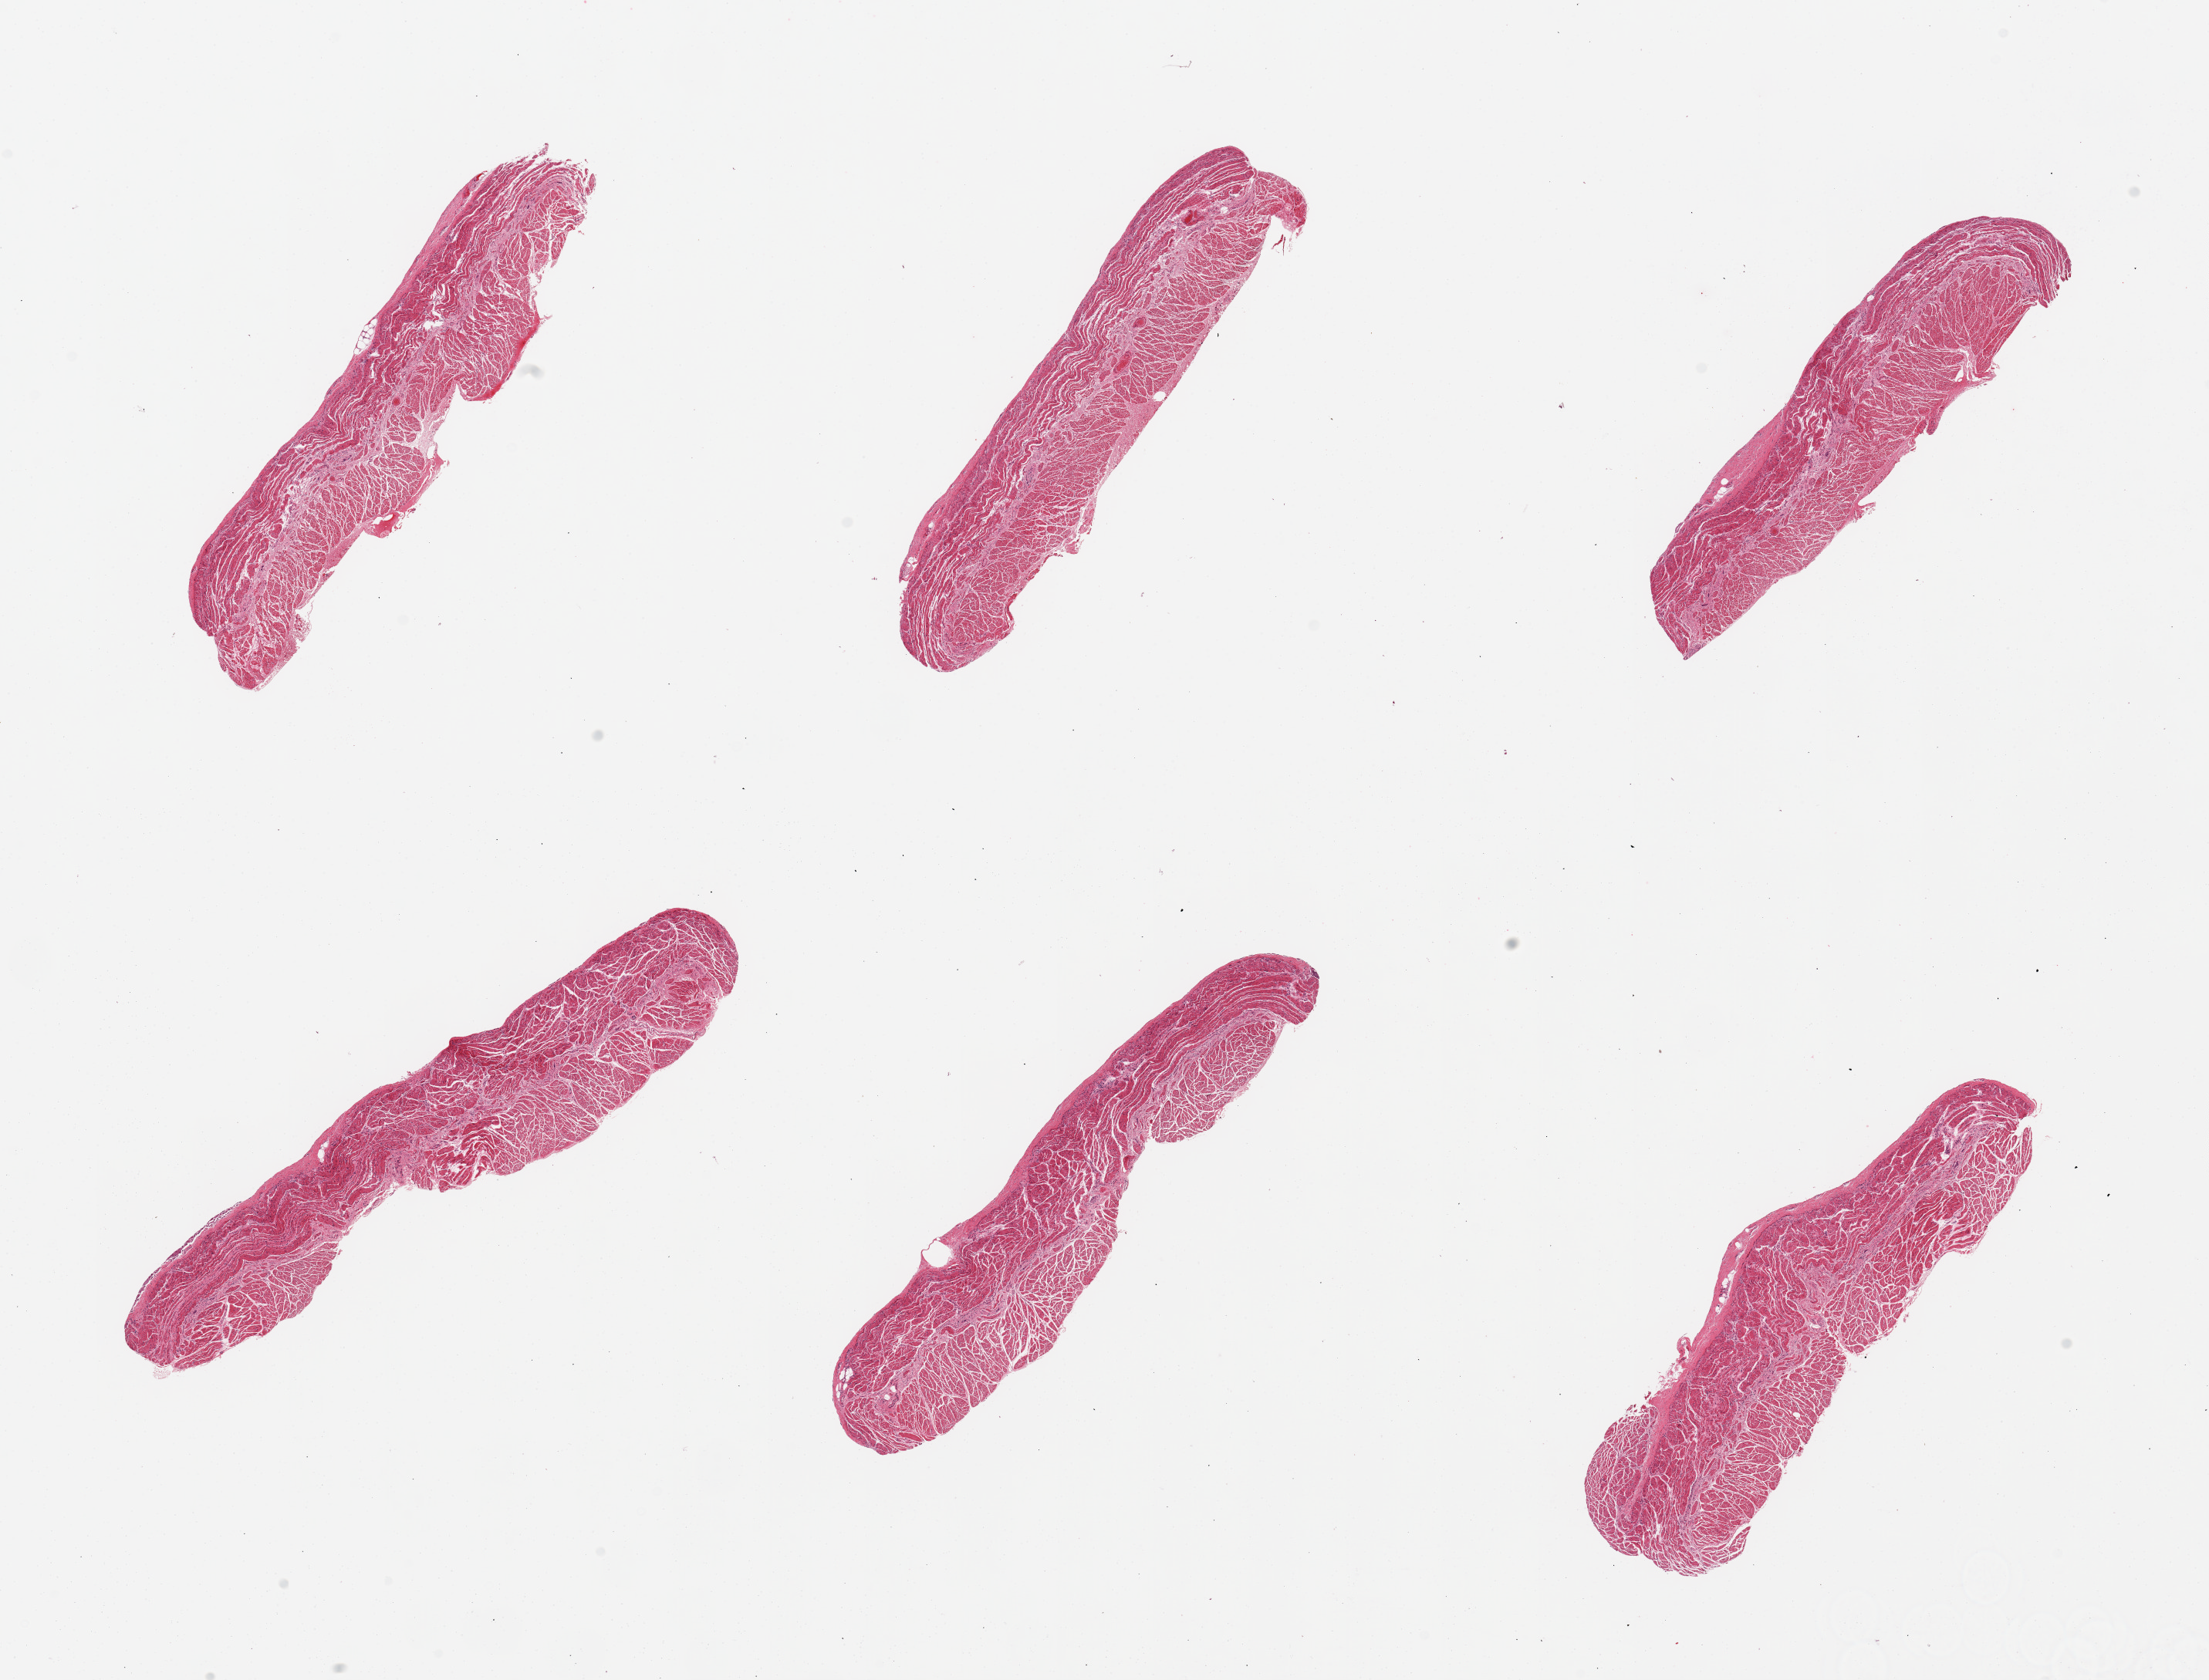
Whole-slide image, hematoxylin and eosin (H&E) stain, a low-resolution overview of the entire scanned area, about 22.6 x 17.2 mm; PAXgene-fixed, paraffin-embedded tissue; target tissue: esophageal muscle; donor tissue sample. Donor sex: male.
Review note (as recorded): 6 pieces; well dissected.